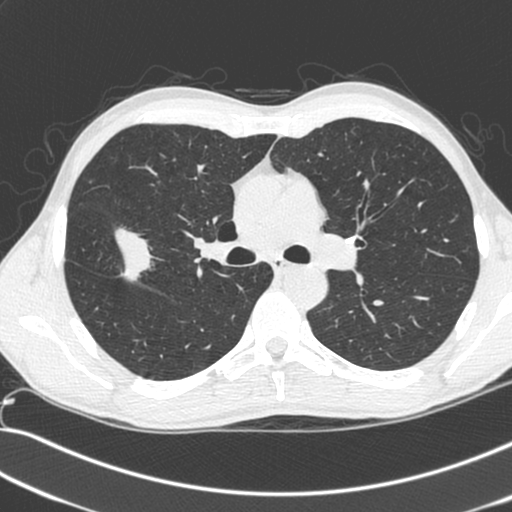
Chest CT (low-dose screening protocol), one axial image; baseline annual screen; lung window (W 1500 / L -600 HU). Male, age 55 years at enrolment. Current smoker at enrolment.
Expert-annotated lung lesion, bounding box <66,217,158,296> (left, top, right, bottom; pixels). Reader record for this screening exam (exam-level; its link to the box is not recorded): non-calcified nodule or mass ≥4 mm, right upper lobe, 52 × 39 mm, spiculated (stellate) margins, soft tissue attenuation. Official screen result: positive, change unspecified: nodule(s) >= 4 mm or enlarging nodule(s), mass(es), or other non-specific abnormalities suspicious for lung cancer. Lung cancer was diagnosed 25 days after this screen: large cell neuroendocrine carcinoma, right upper lobe, poorly differentiated (G3), stage IIB (AJCC 6th edition), 49 mm at pathology.